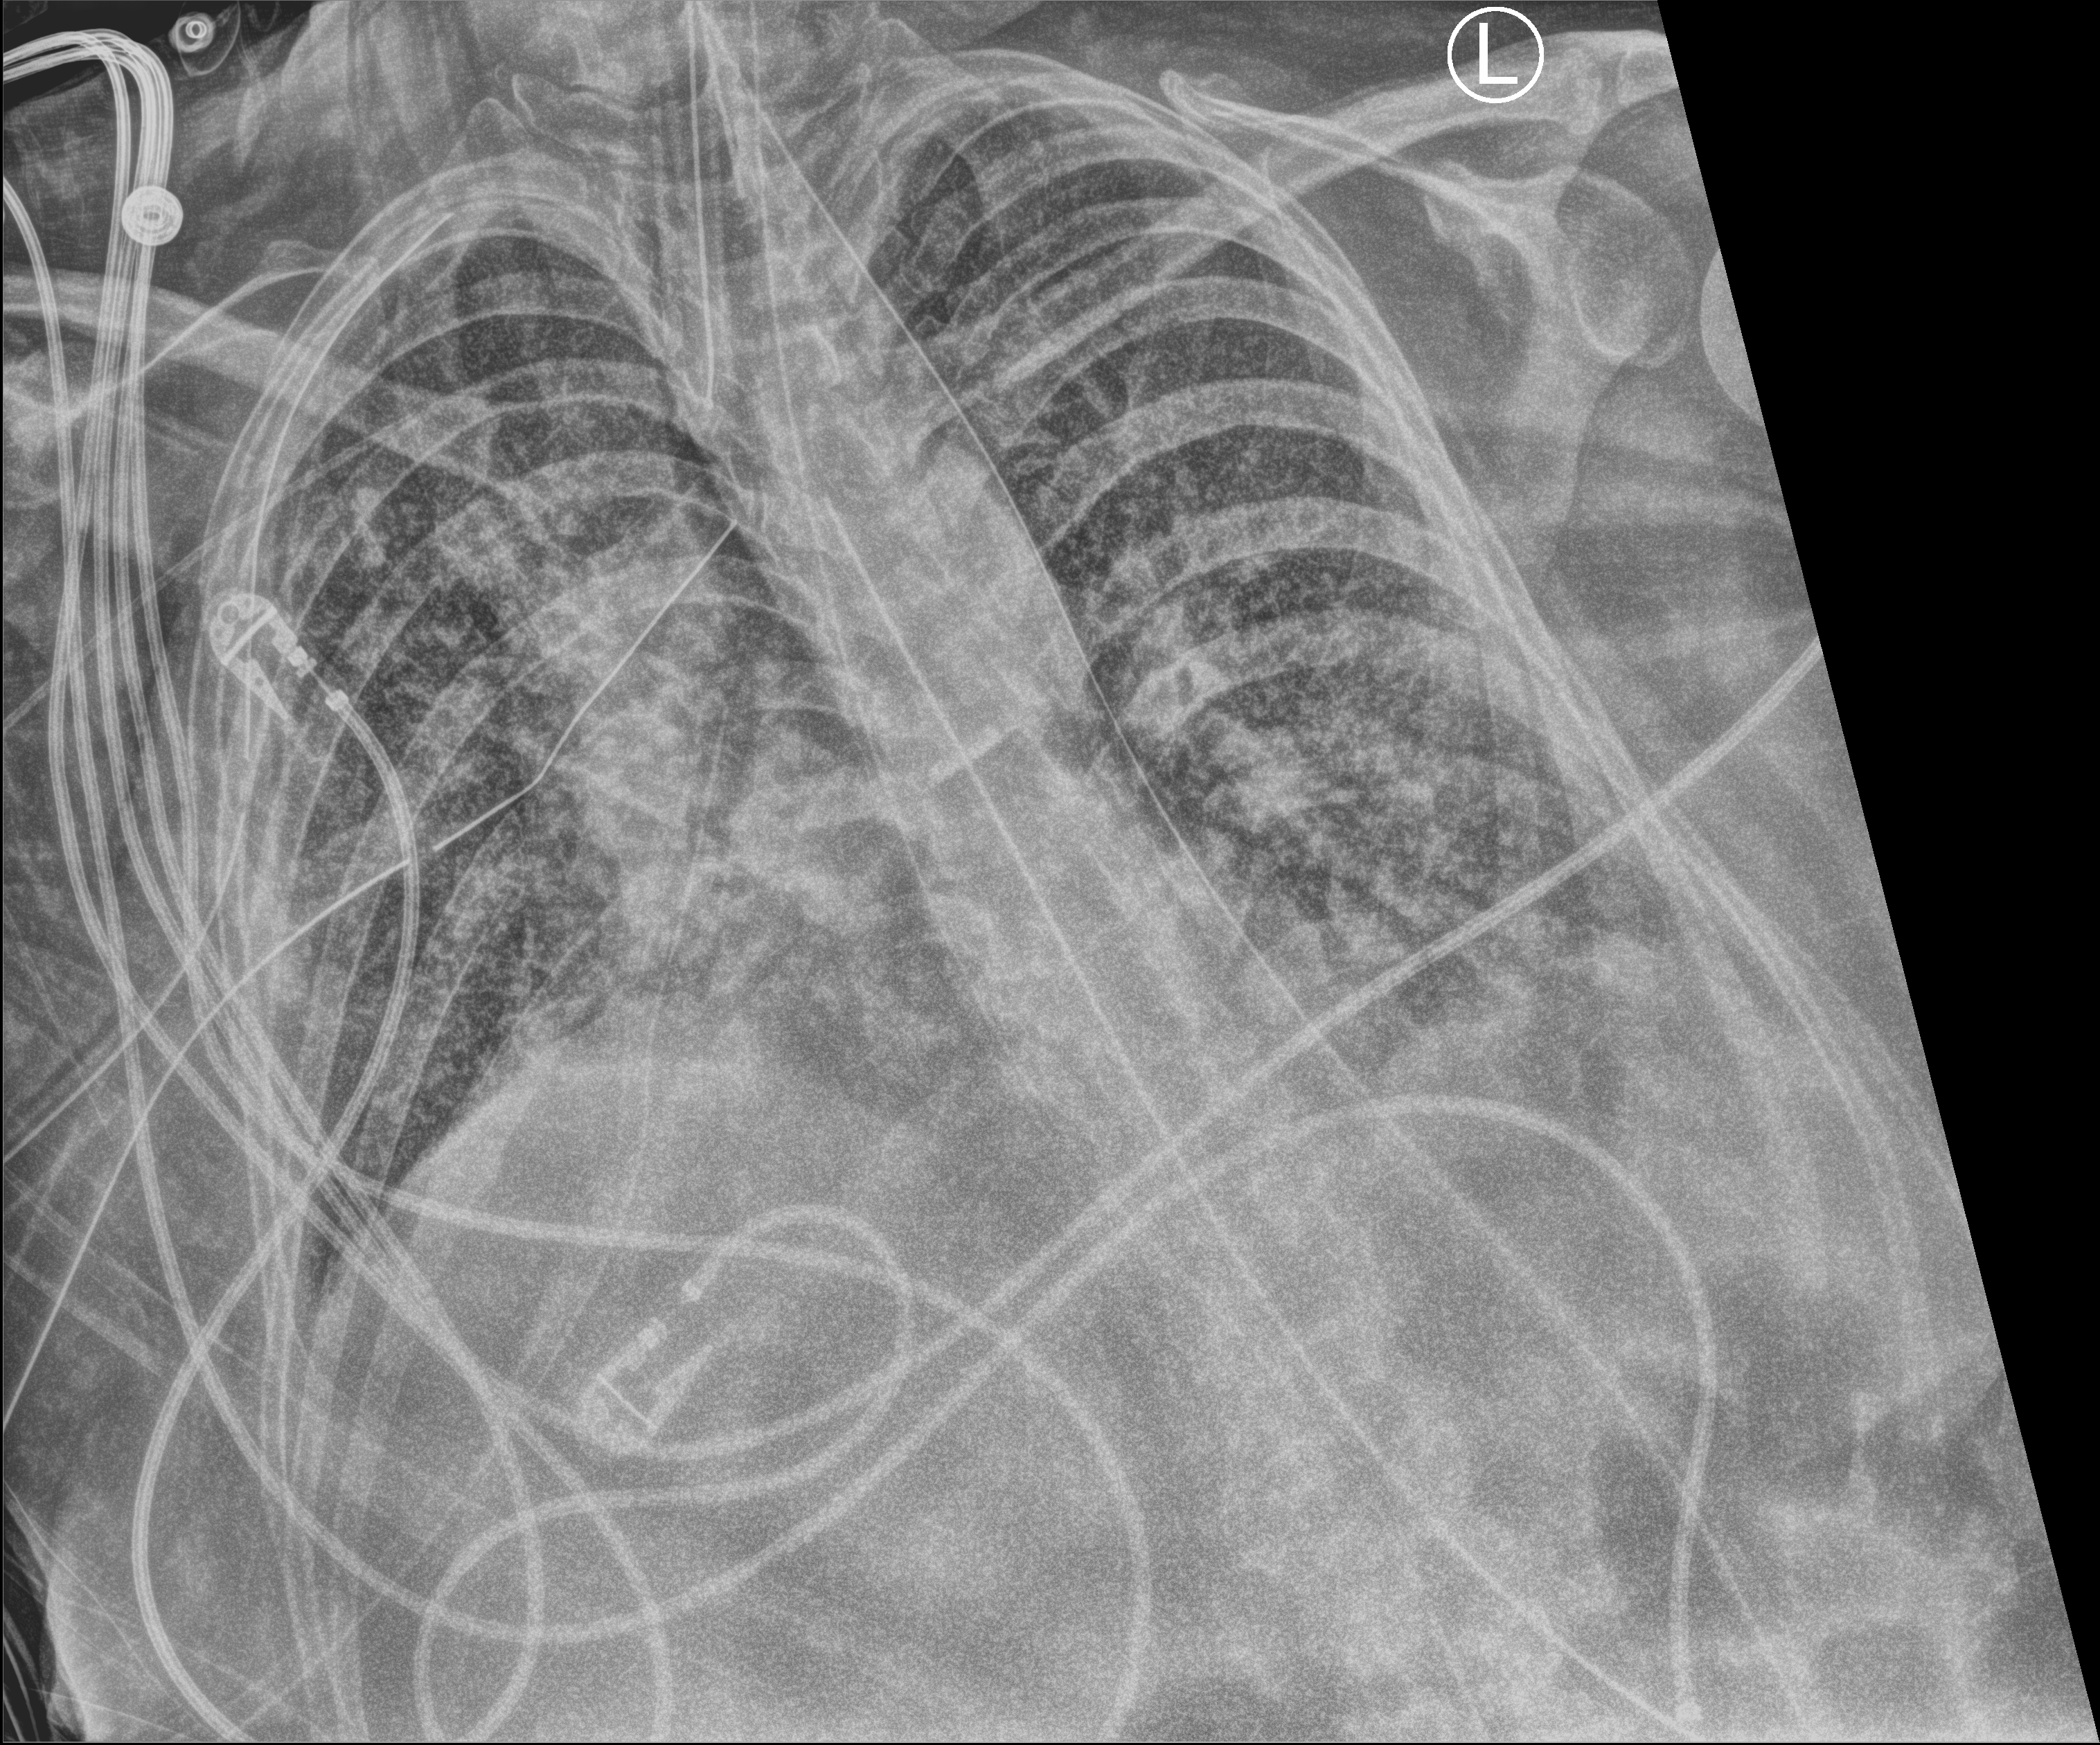
Portable chest radiograph; anteroposterior (AP) projection. Patient hospitalised with COVID-19, aged 18–59 years.
From the hospital-stay record, not from the radiograph (when in the stay this image was taken is not recorded):
- mechanically ventilated during this hospital stay: yes
- other chronic lung disease (admission record): no
- admitted to intensive care during this hospital stay: yes